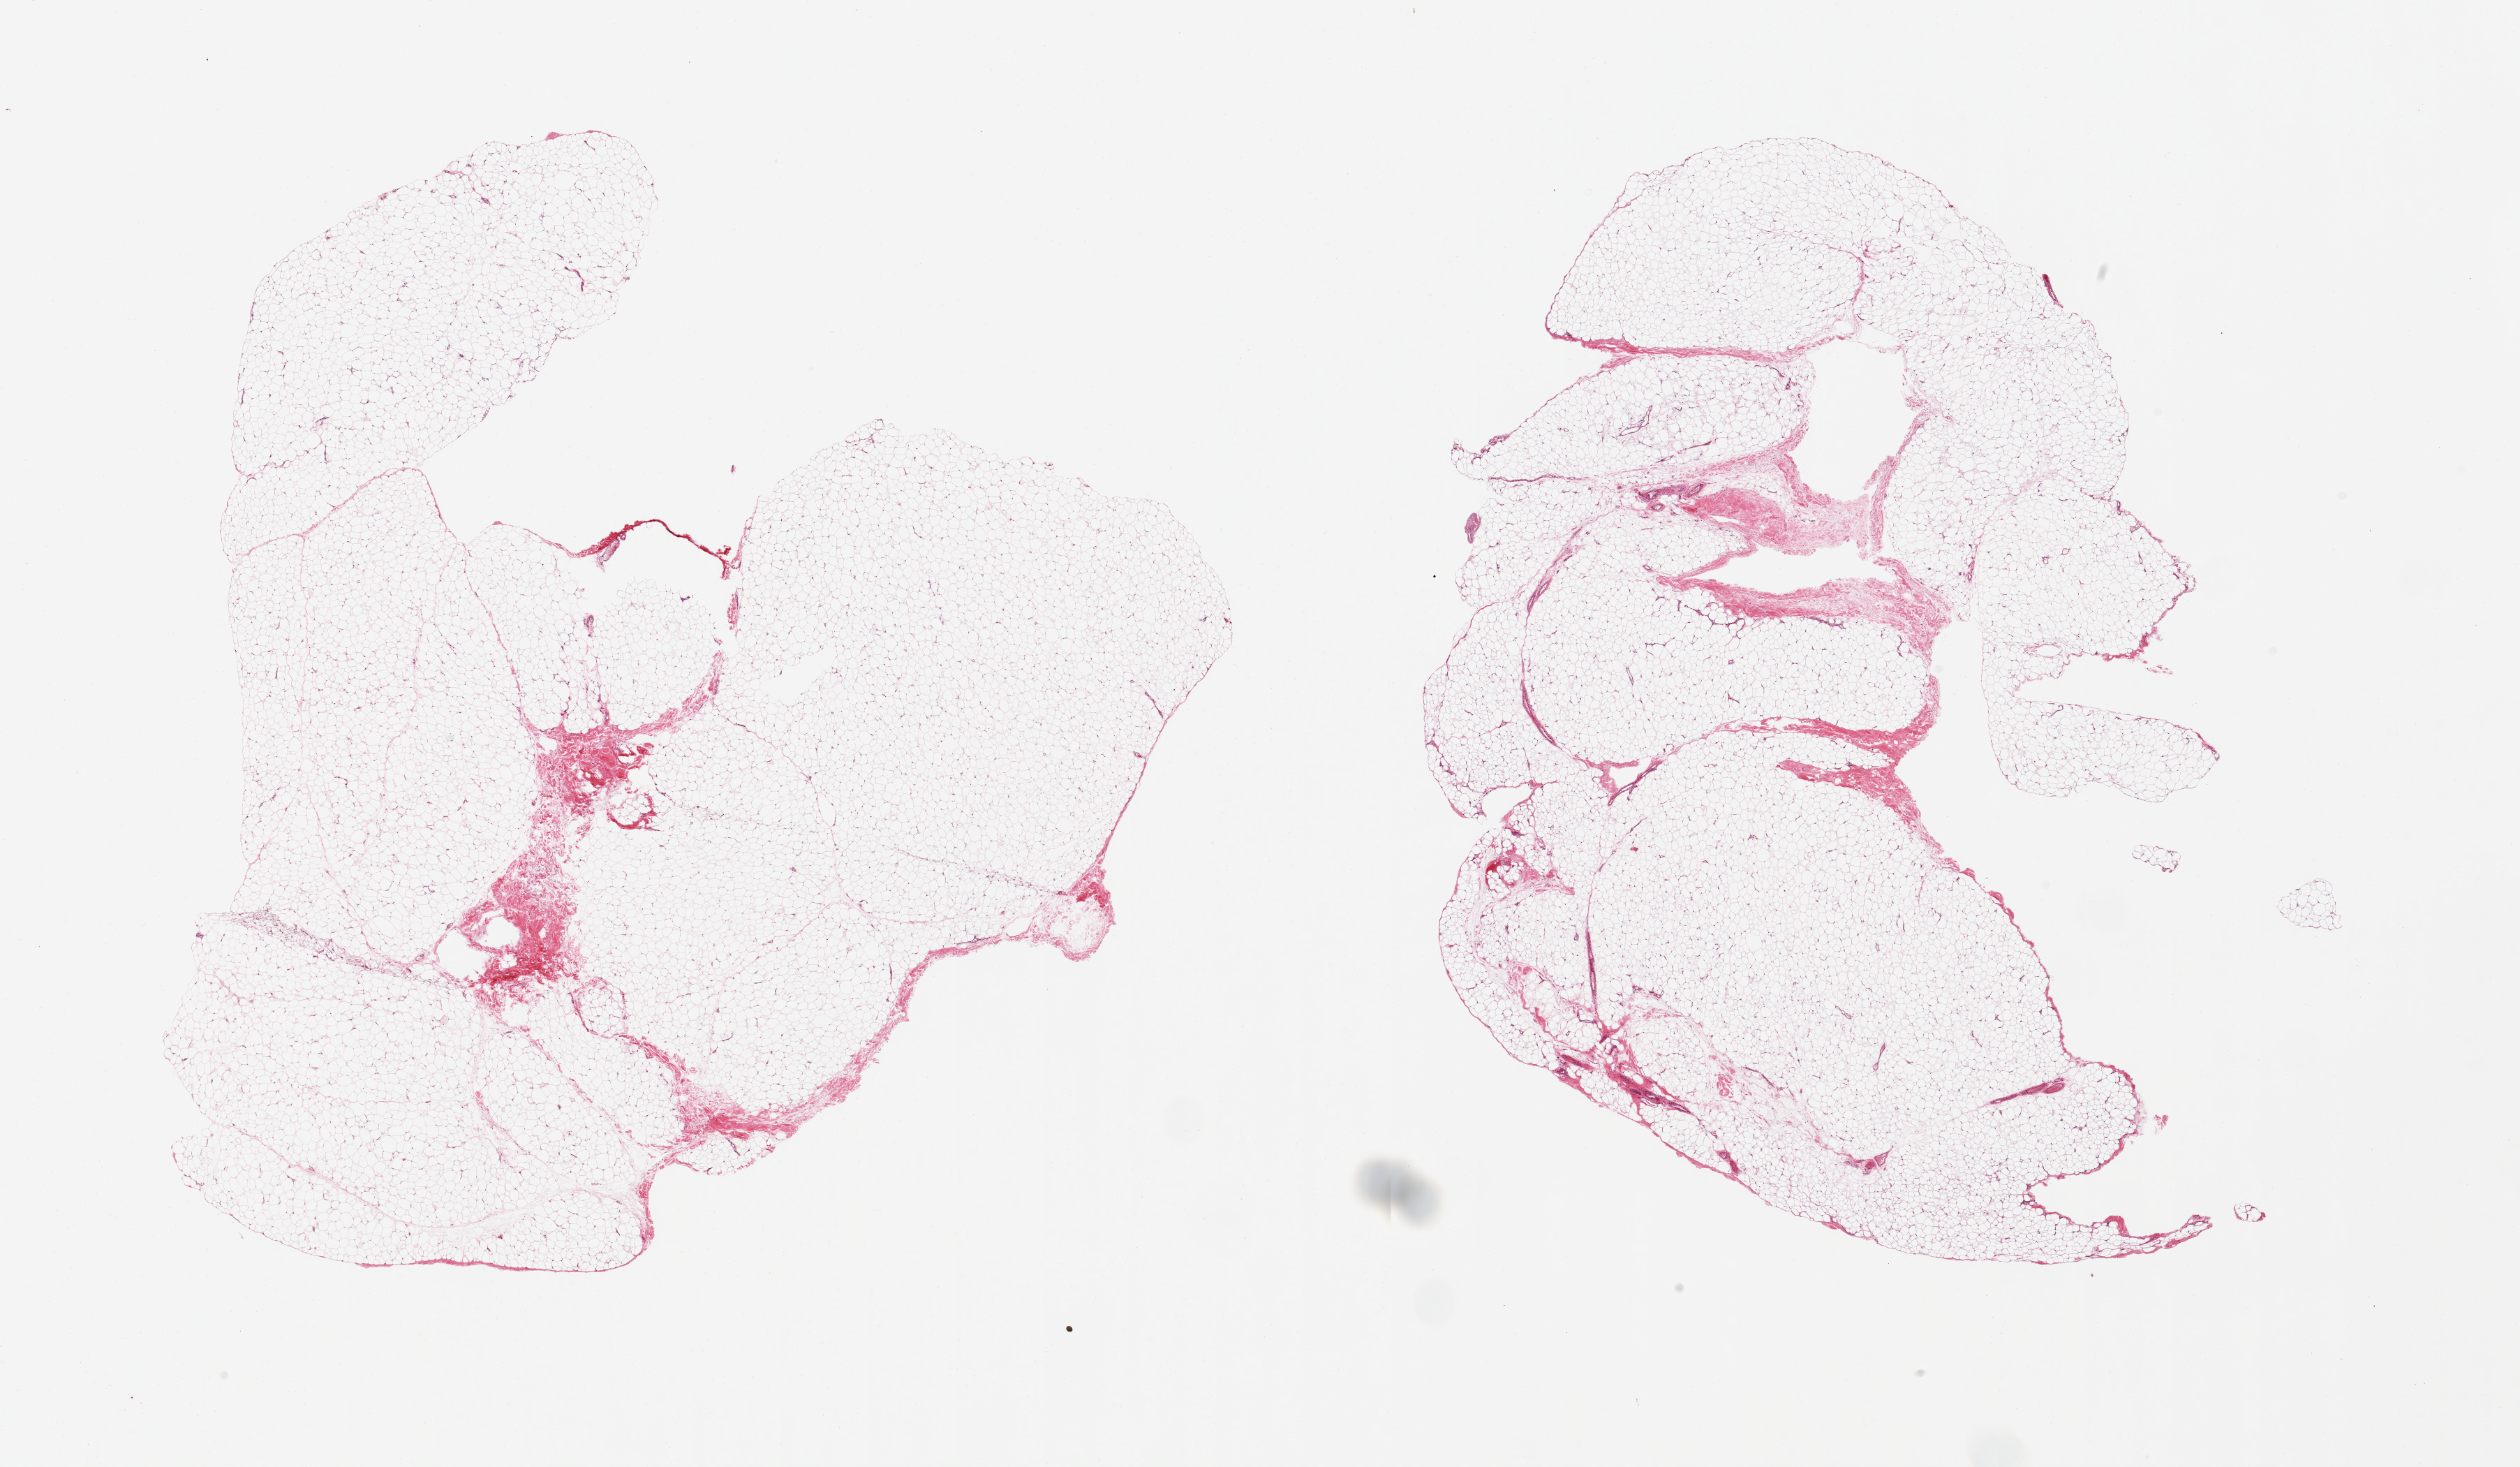
Haematoxylin and eosin whole-slide image, brightfield, low-resolution overview of the scanned area, about 28.5 x 16.6 mm; PAXgene-fixed paraffin-embedded (PFPE) section; target tissue: adipose tissue; tissue donor sample. Donor: male.
Reviewer comment on this tissue sample: 2 pieces, ~10-15% interstital fascia/fibrous tissue.